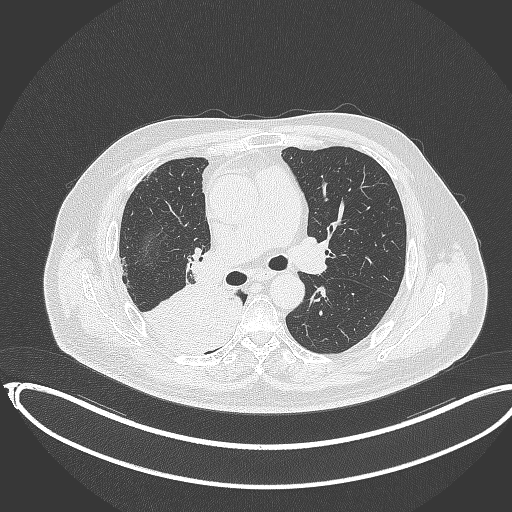
Chest CT, one axial slice; position 210 of 403 along the scan axis; reconstruction kernel B70f; lung window (W 1500 / L -600 HU); 512 × 512 image matrix. Male patient, age 68 years. From the clinical record (not read from this slice): clinical TNM (as recorded): T2a N0 M0.
Outlined on this slice (bounding box drawn by a radiologist):
- lung tumour (recorded histology: adenocarcinoma): bounding box <143,283,245,354> (left, top, right, bottom; pixels)